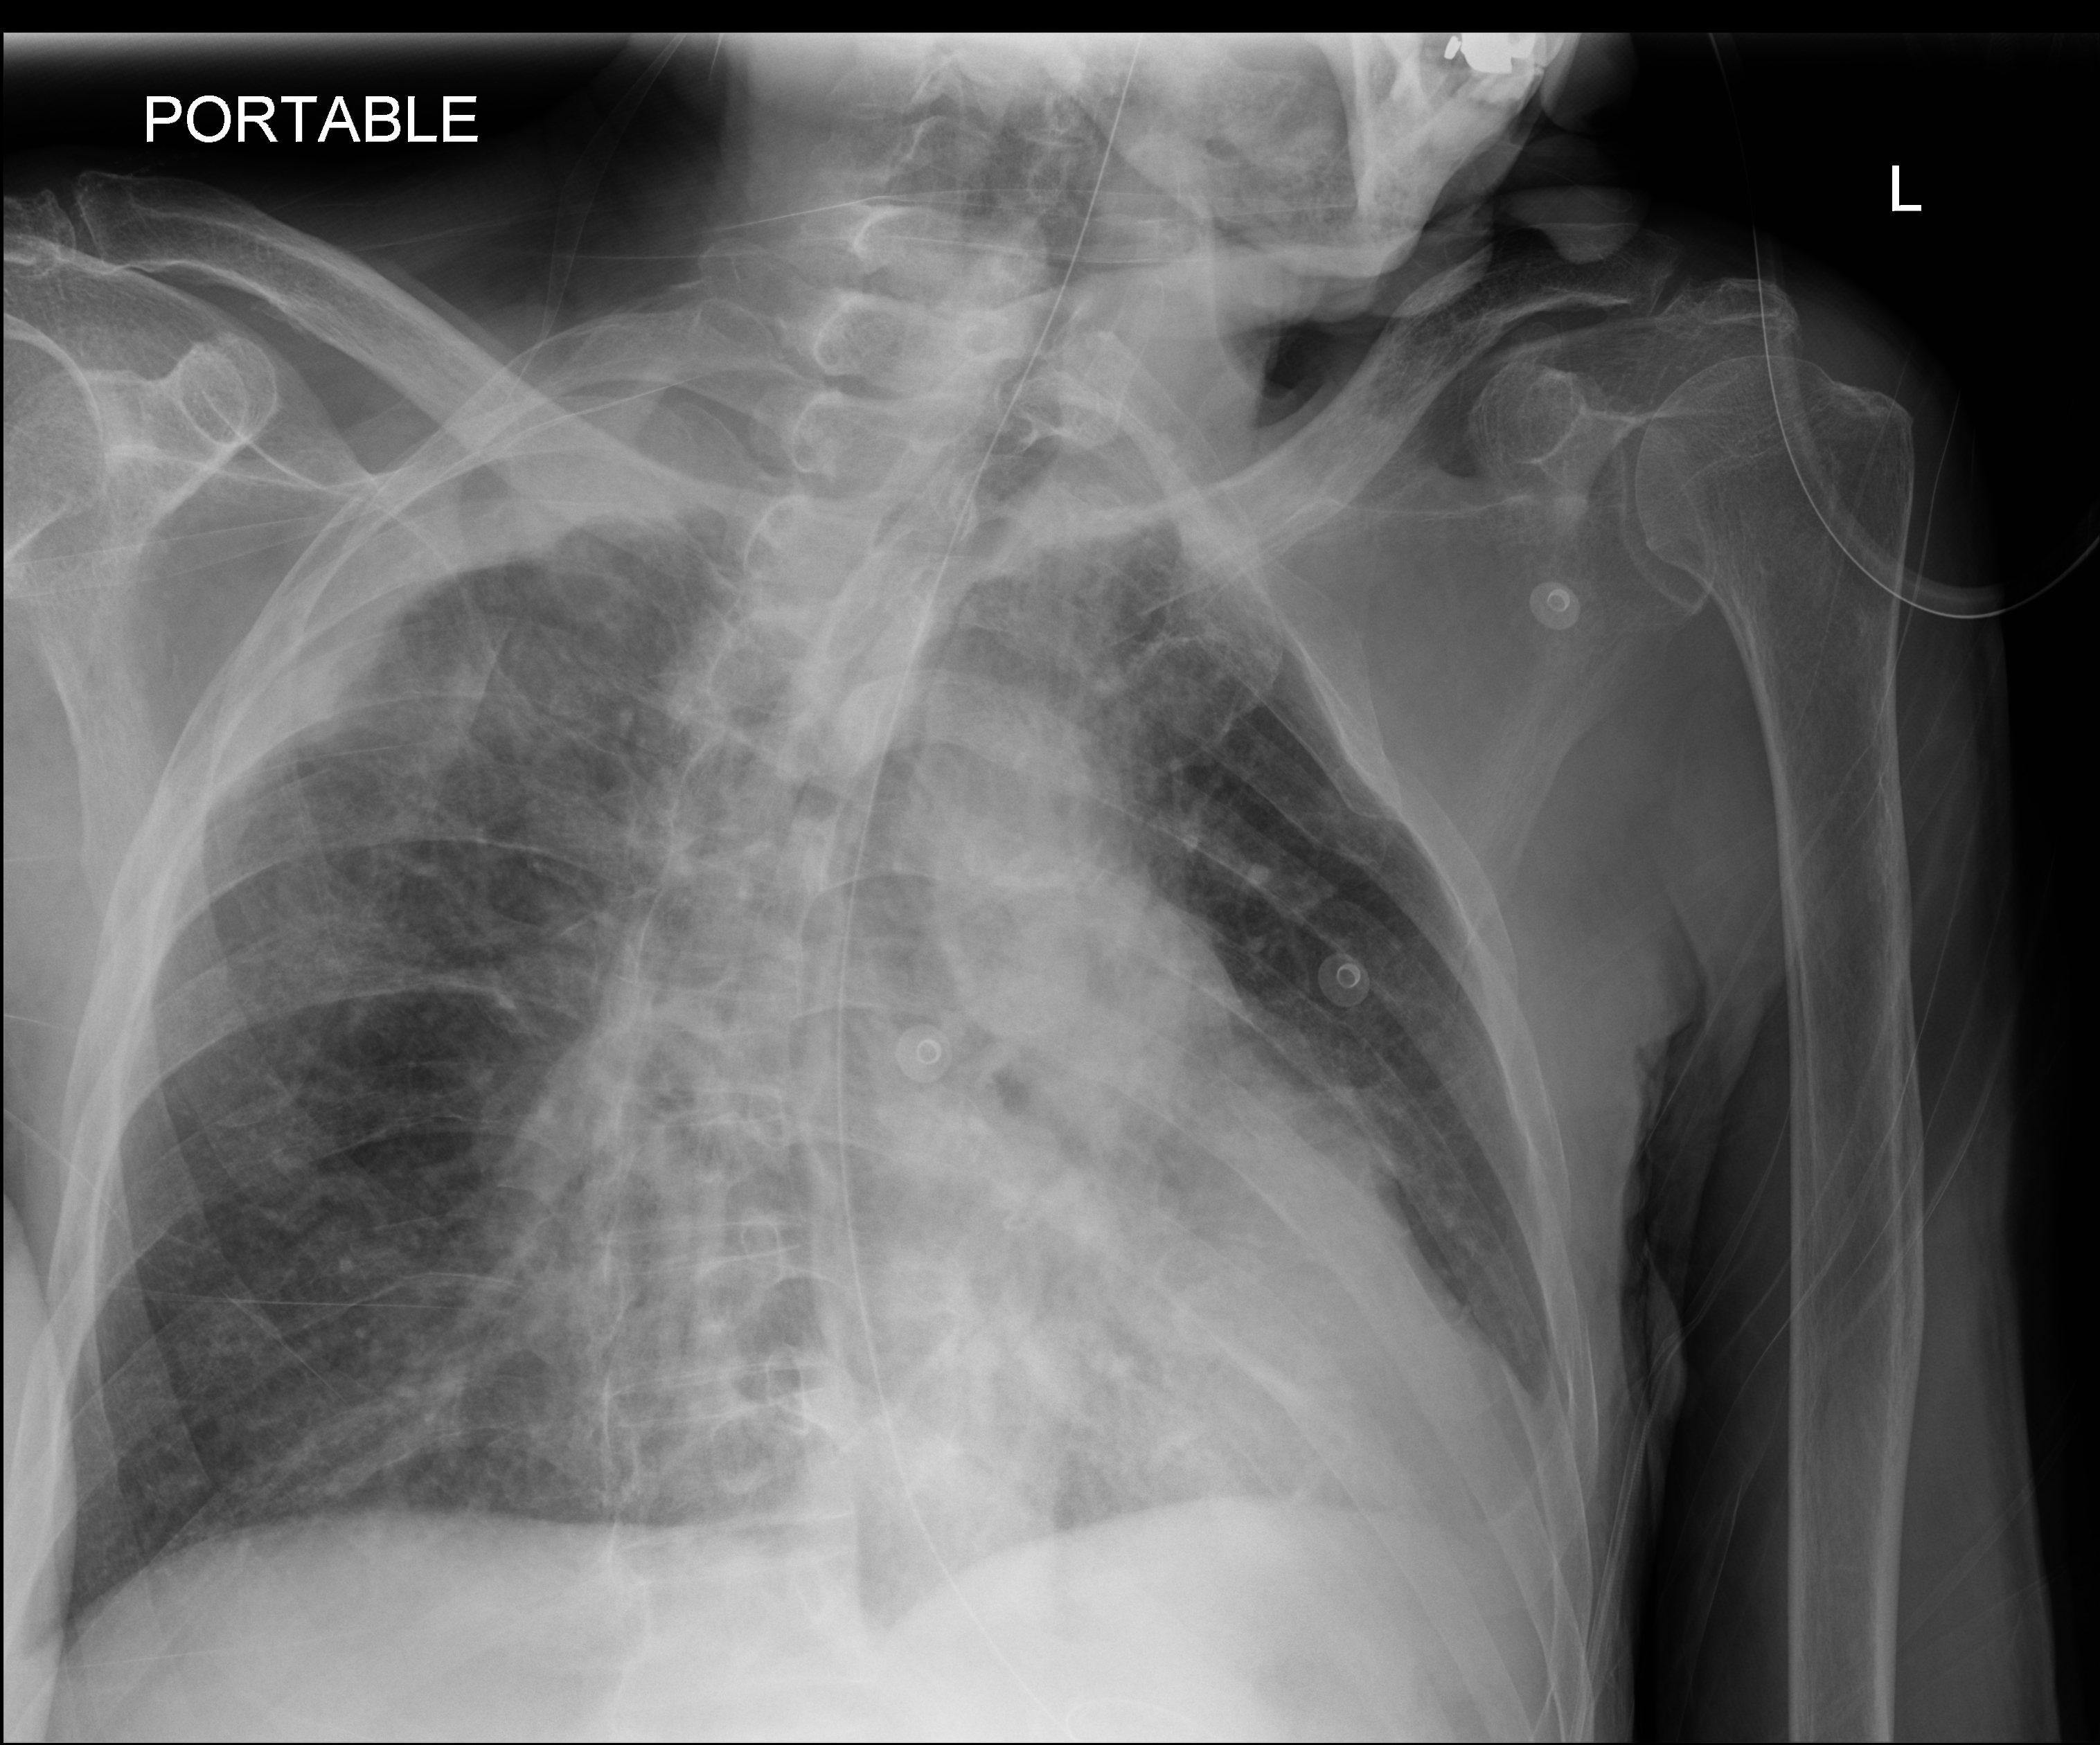
Chest X-ray (portable); anteroposterior (AP) projection. Male patient hospitalised with COVID-19, age 75–90 years.
Hospital-stay facts (about this admission, not read from this image; timing relative to this image not recorded):
- other chronic lung disease (admission record): no
- admitted to intensive care during this hospital stay: no